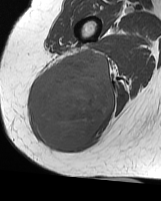
MRI of an extremity soft-tissue mass, one axial slice. Slice 29 of 70 in the series (ordered by position). MR volume resampled by the dataset authors to the PET/CT grid (not the native acquisition matrix). 3.27 mm slice thickness. 161 × 201 image matrix, field of view 157 × 196 mm. Female patient. From the clinical record (not read from this slice): histological type: synovial sarcoma; grade: intermediate; site of the primary tumour: right buttock.
Structures marked on this image (expert contour drawn on MRI and transferred to this co-registered scan by the dataset authors):
- gross tumour volume including surrounding oedema: box from (x=31, y=51) to (x=116, y=153) px
- gross tumour volume (mass): (x=31, y=51)–(x=116, y=153)